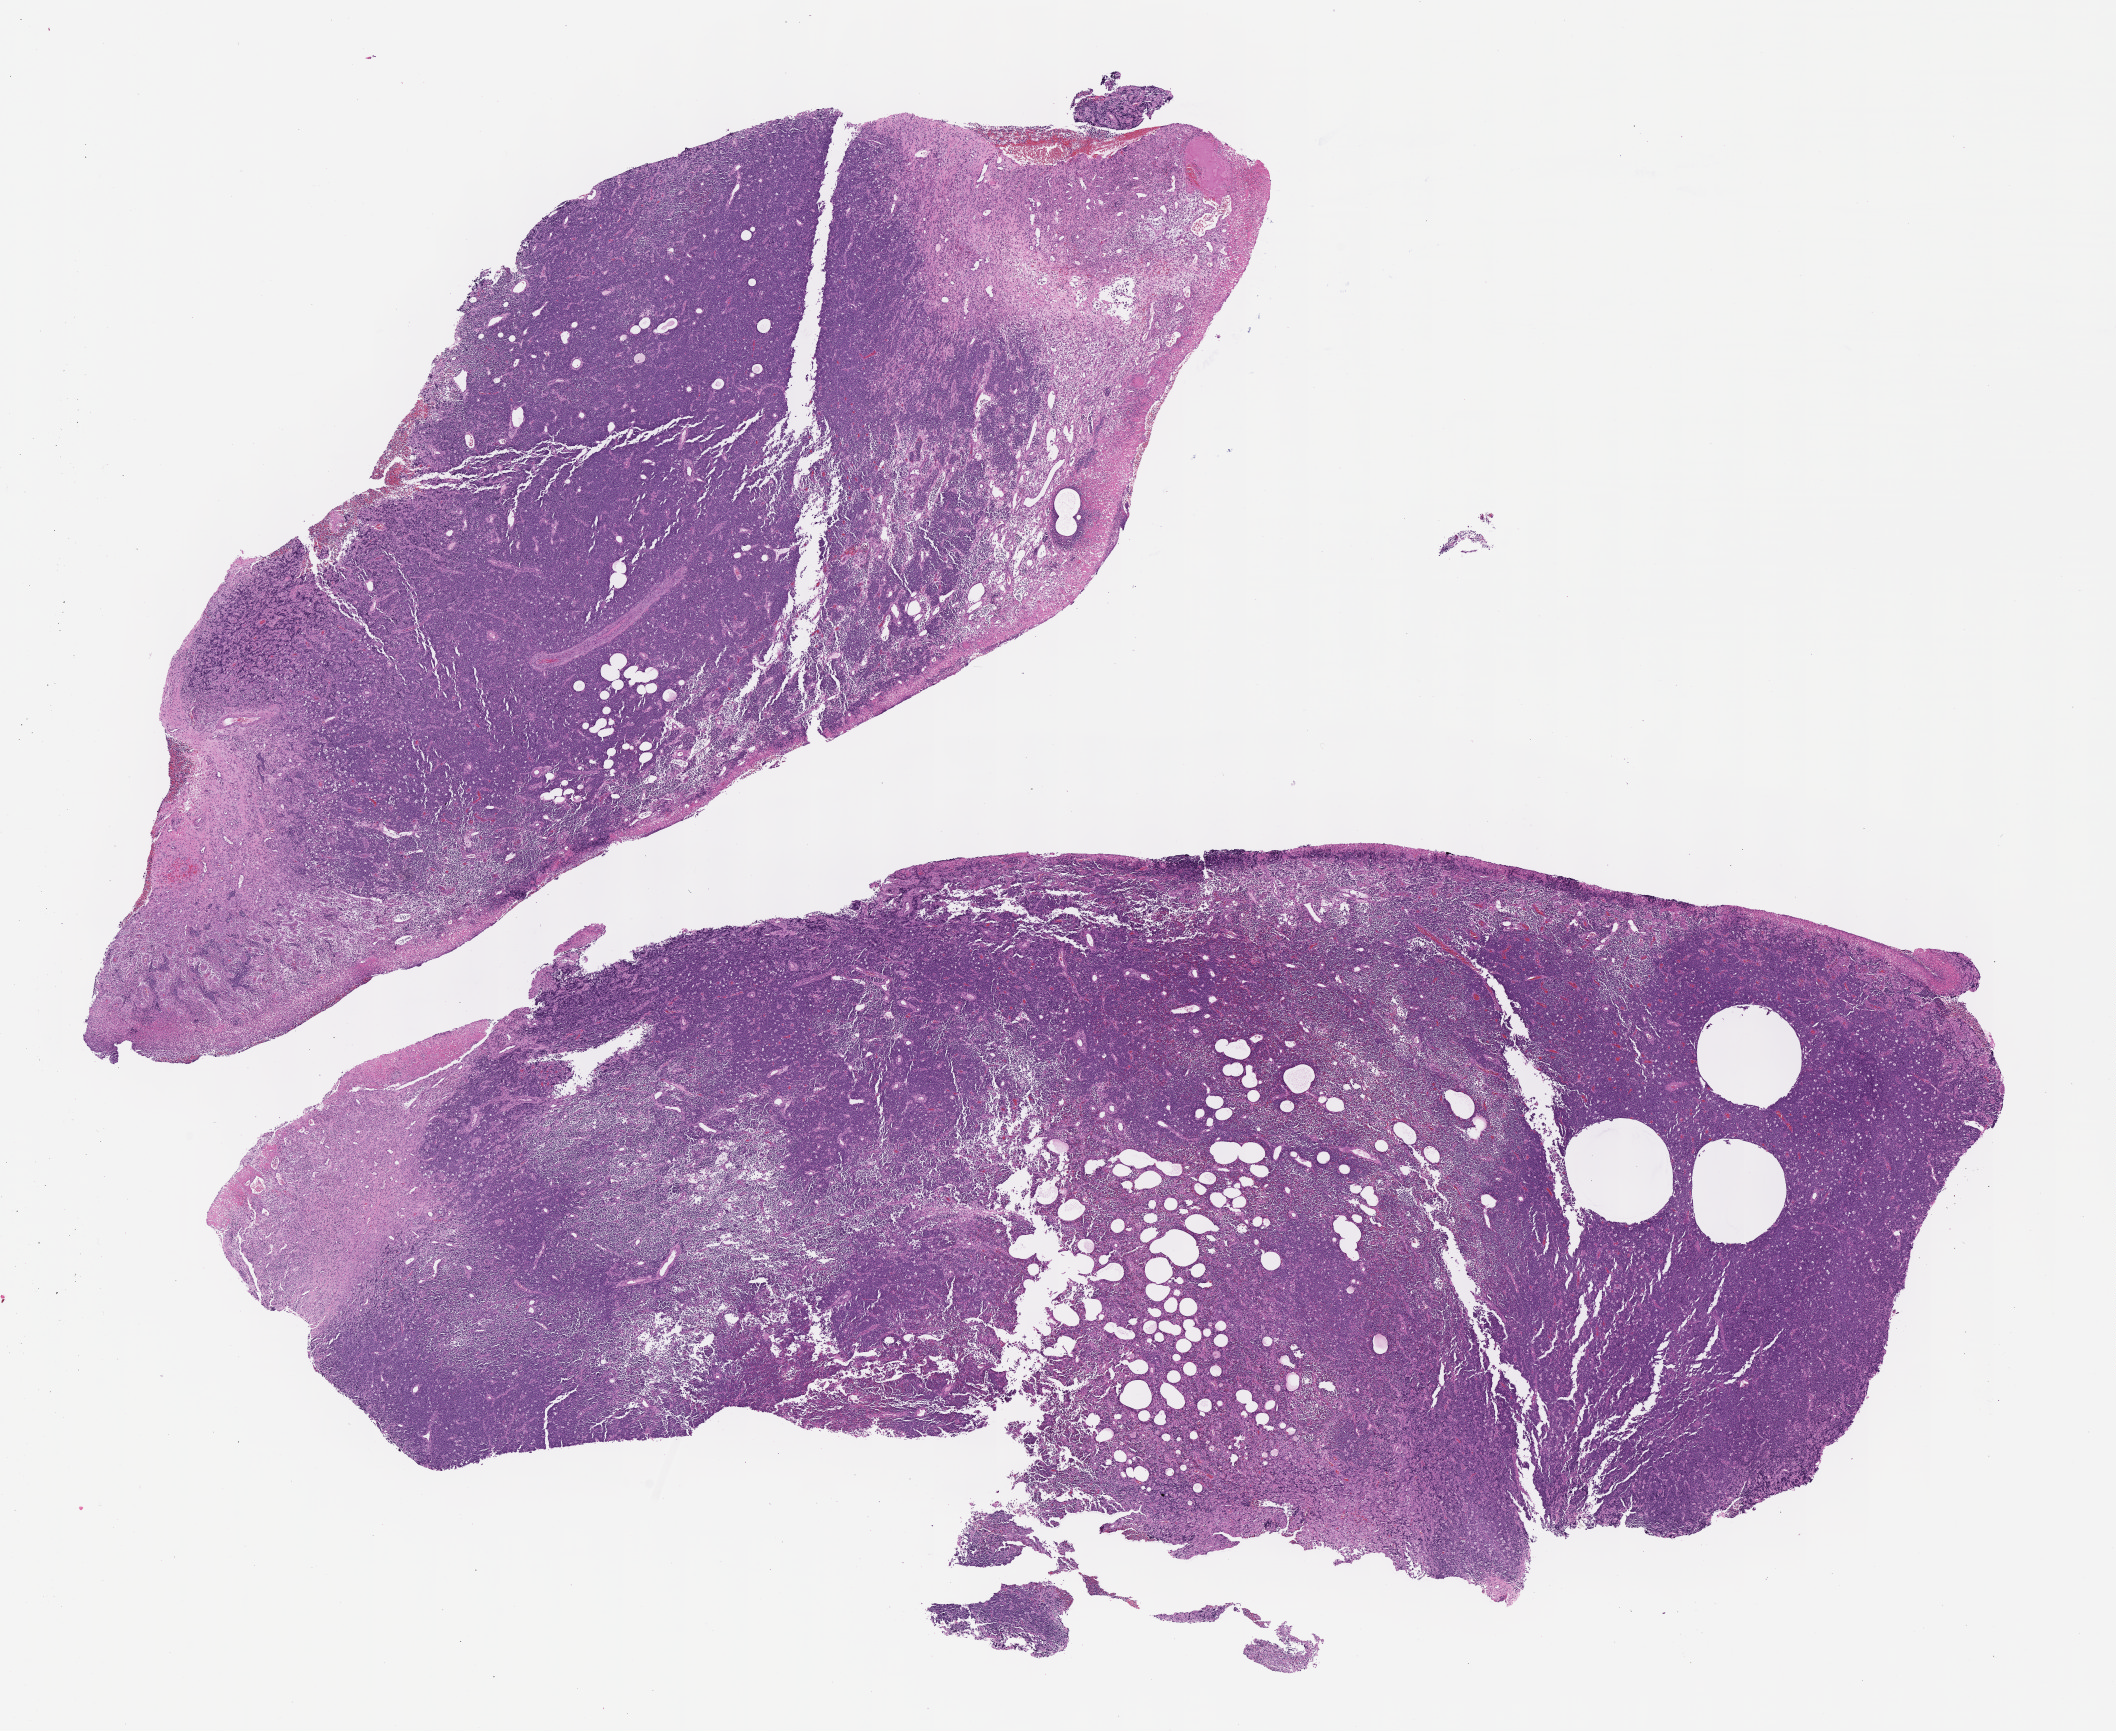
Digitized H&E-stained section — whole scanned area (about 17.1 x 14.0 mm) shown as a low-resolution overview; formalin-fixed, paraffin-embedded (FFPE) tissue; specimen: primary tumor; site: cranium. Female patient; age at initial diagnosis 6 years. Composition of this section per pathologist review: tumor cells 80%, tumor nuclei 90%, stromal cells 5%, necrosis 5%, normal cells 10%. Infiltration values recorded for this section: lymphocyte infiltration 50%, monocyte infiltration 30%, neutrophil infiltration 5%.
Ann Arbor stage (patient): Stage III. Section: bottom of the tissue portion. Histologic diagnosis: Burkitt lymphoma, NOS.